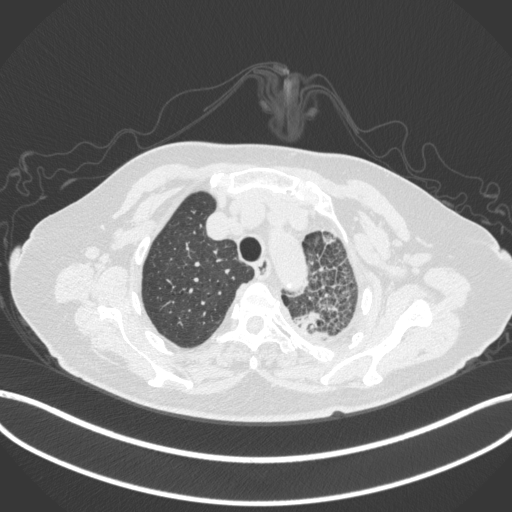
Chest CT, one axial slice. Position 322 of 399 along the scan axis. Reconstruction kernel B31f. 120 kVp. Lung window (W 1500 / L -600 HU). 1 mm slice thickness. 512 × 512 image matrix, field of view 400 × 400 mm. Patient: female, 75 years. From the clinical record (not read from this slice): clinical TNM (as recorded): T3 N3 M1.
Annotated regions visible in this slice (rectangle marked by the reading radiologist):
- lung tumour (recorded histology: adenocarcinoma): bounding box (x1, y1, x2, y2) in pixels: (290, 304, 337, 341)